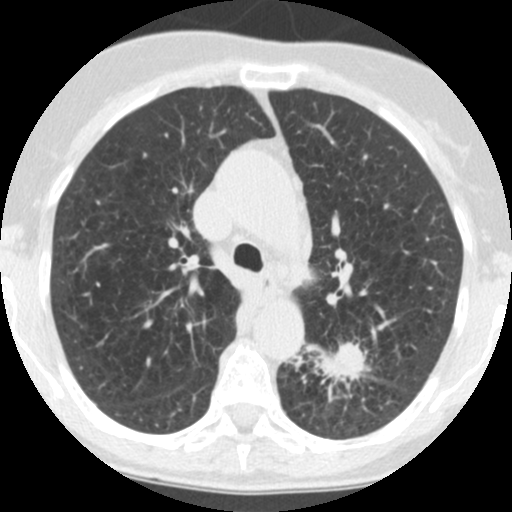
Axial slice from a low-dose chest CT screening exam, third annual screen, lung window (W 1500 / L -600 HU), 2.5 mm slice thickness, standard (soft-tissue) reconstruction kernel (STANDARD). Female participant, aged 71 years at enrolment.
- Lesion marked by an expert reader, bounding box <296,333,379,411> (left, top, right, bottom; pixels).
- The screening reader recorded 2 non-calcified nodules or masses ≥4 mm on this exam; which of them this box marks is not recorded.
- Official screen result: positive, other.
- Lung cancer was diagnosed 26 days after this screen: squamous cell carcinoma, NOS, left lower lobe, poorly differentiated (G3), stage IB (AJCC 6th edition), 40 mm at pathology.